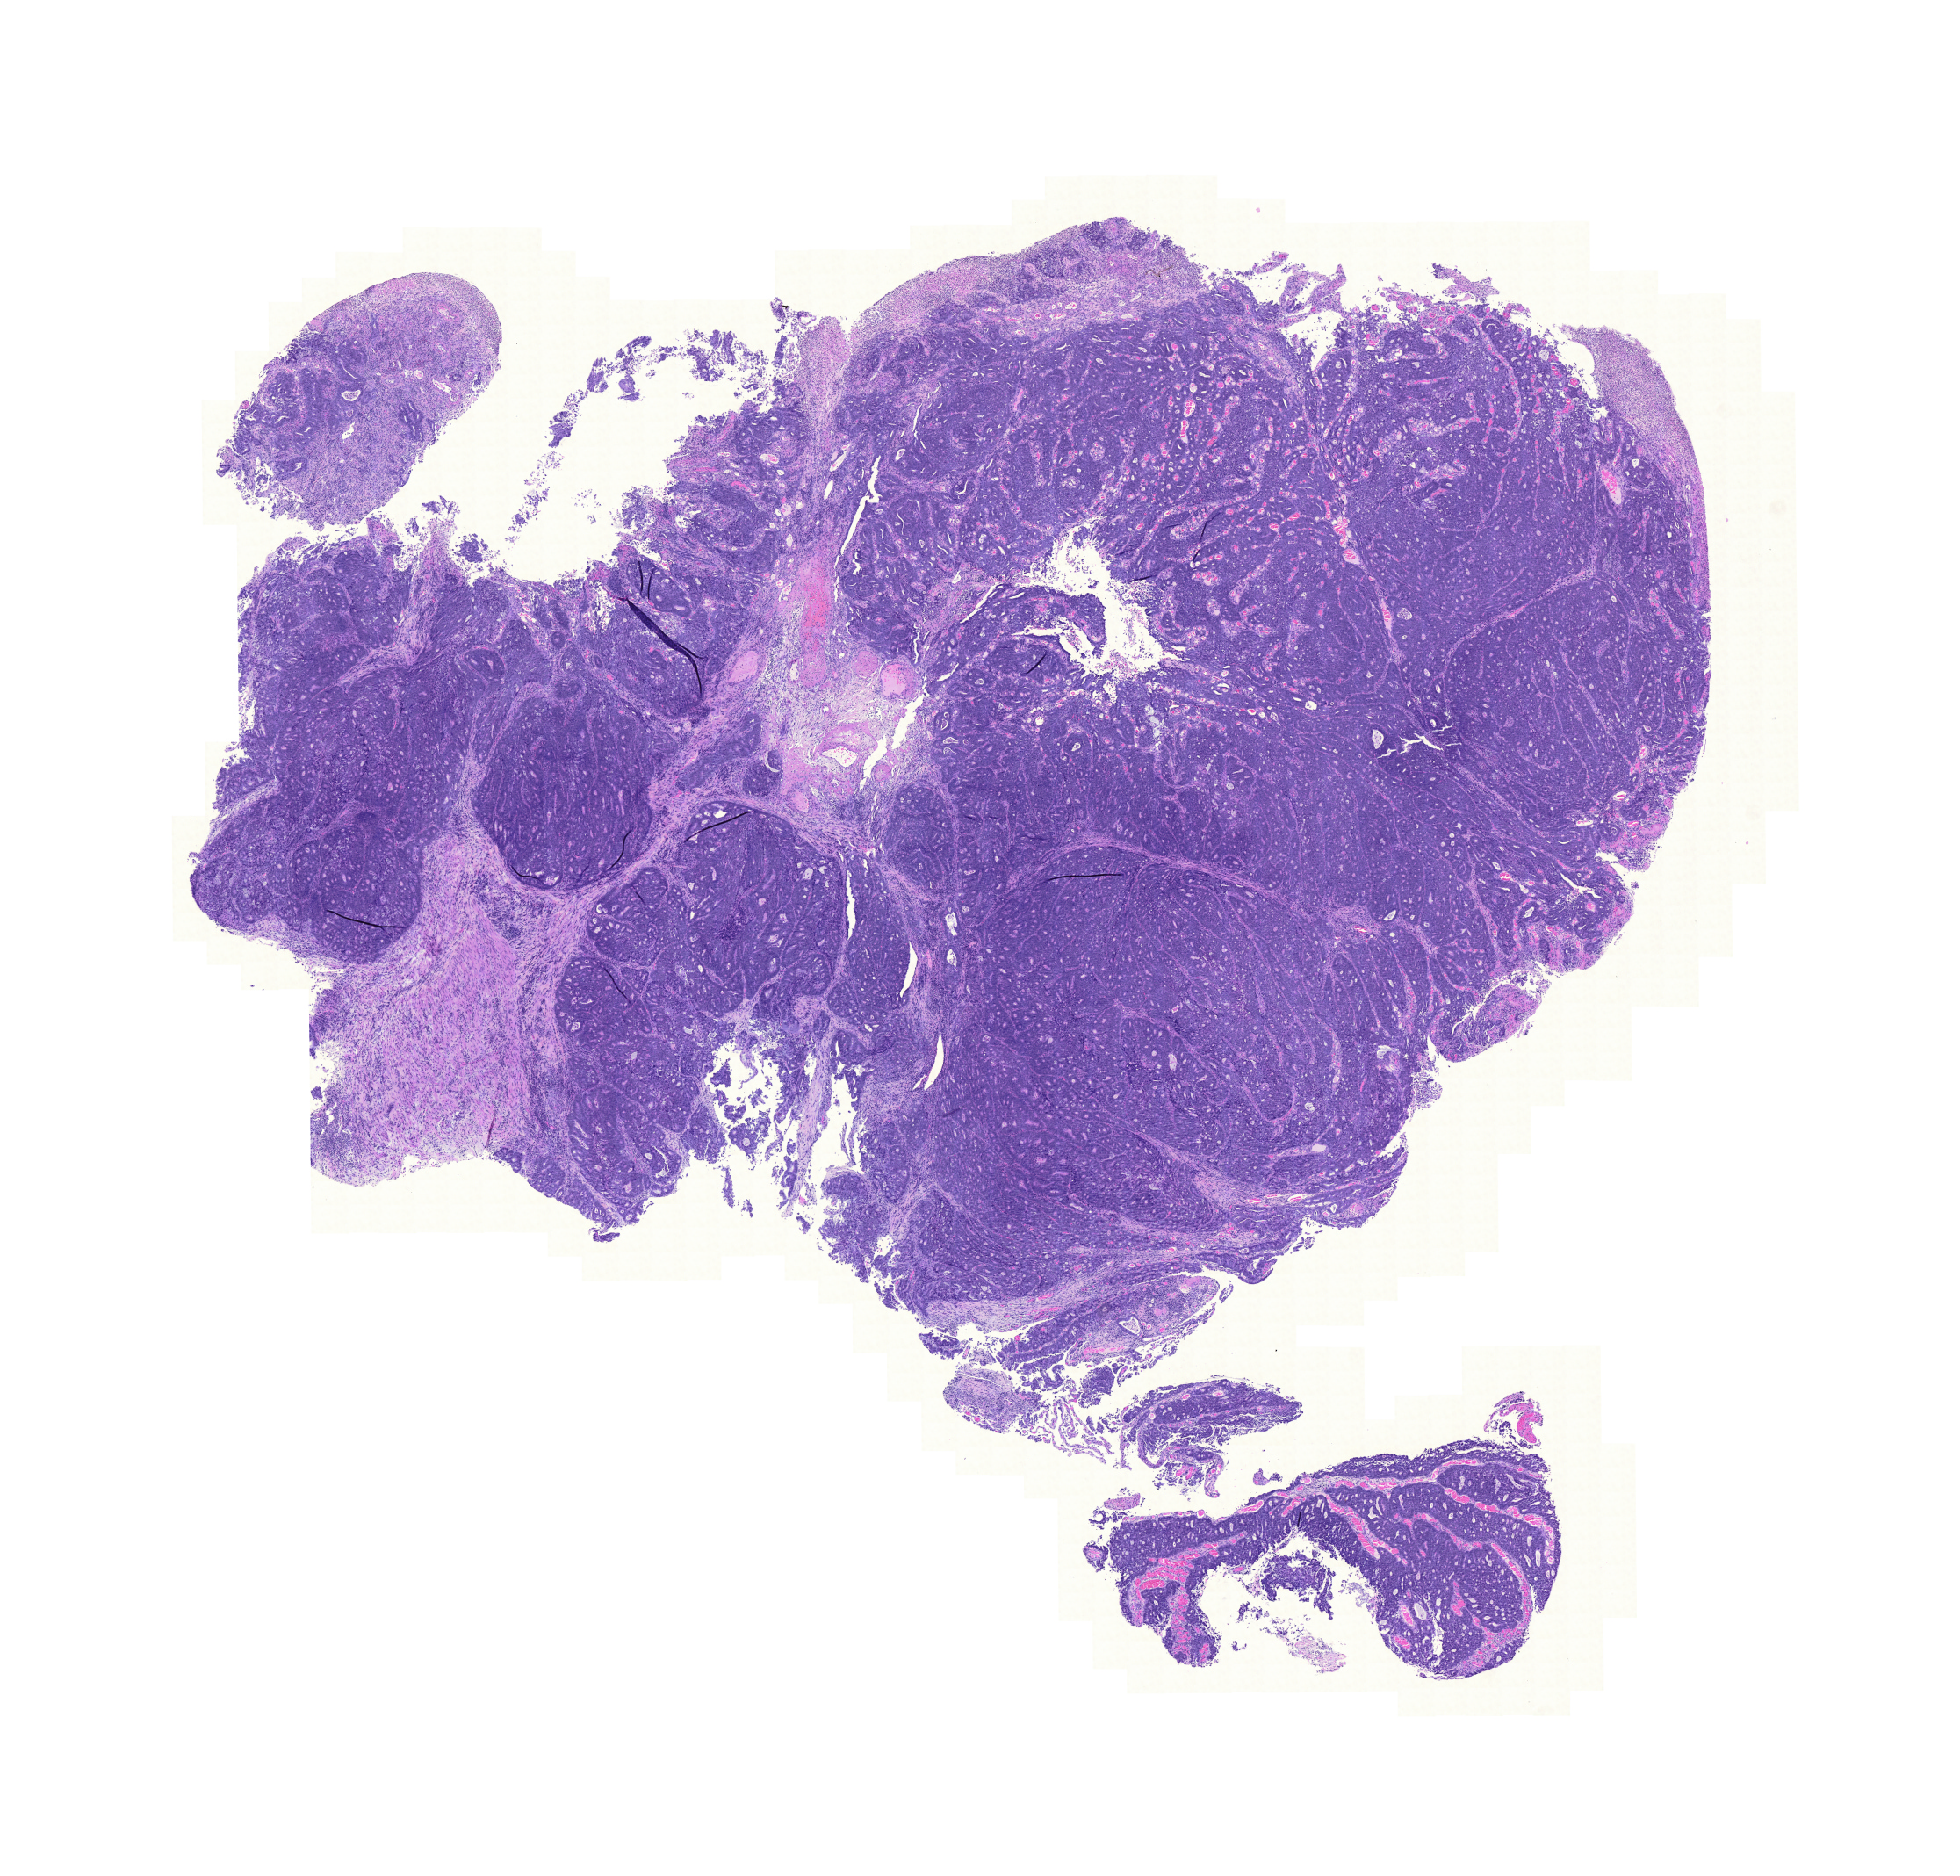
Whole-slide histology image, Hematoxylin and eosin (H&E) stained — shown as a low-resolution overview of the whole scanned area (about 16.6 x 15.9 mm), formalin-fixed paraffin-embedded (FFPE) diagnostic section, colon, primary tumour sample. Female patient; age at initial diagnosis 46 years.
Pathologic diagnosis: Adenocarcinoma, NOS. AJCC pathologic stage: IIB (6th edition). TNM: T4 N0 M0.